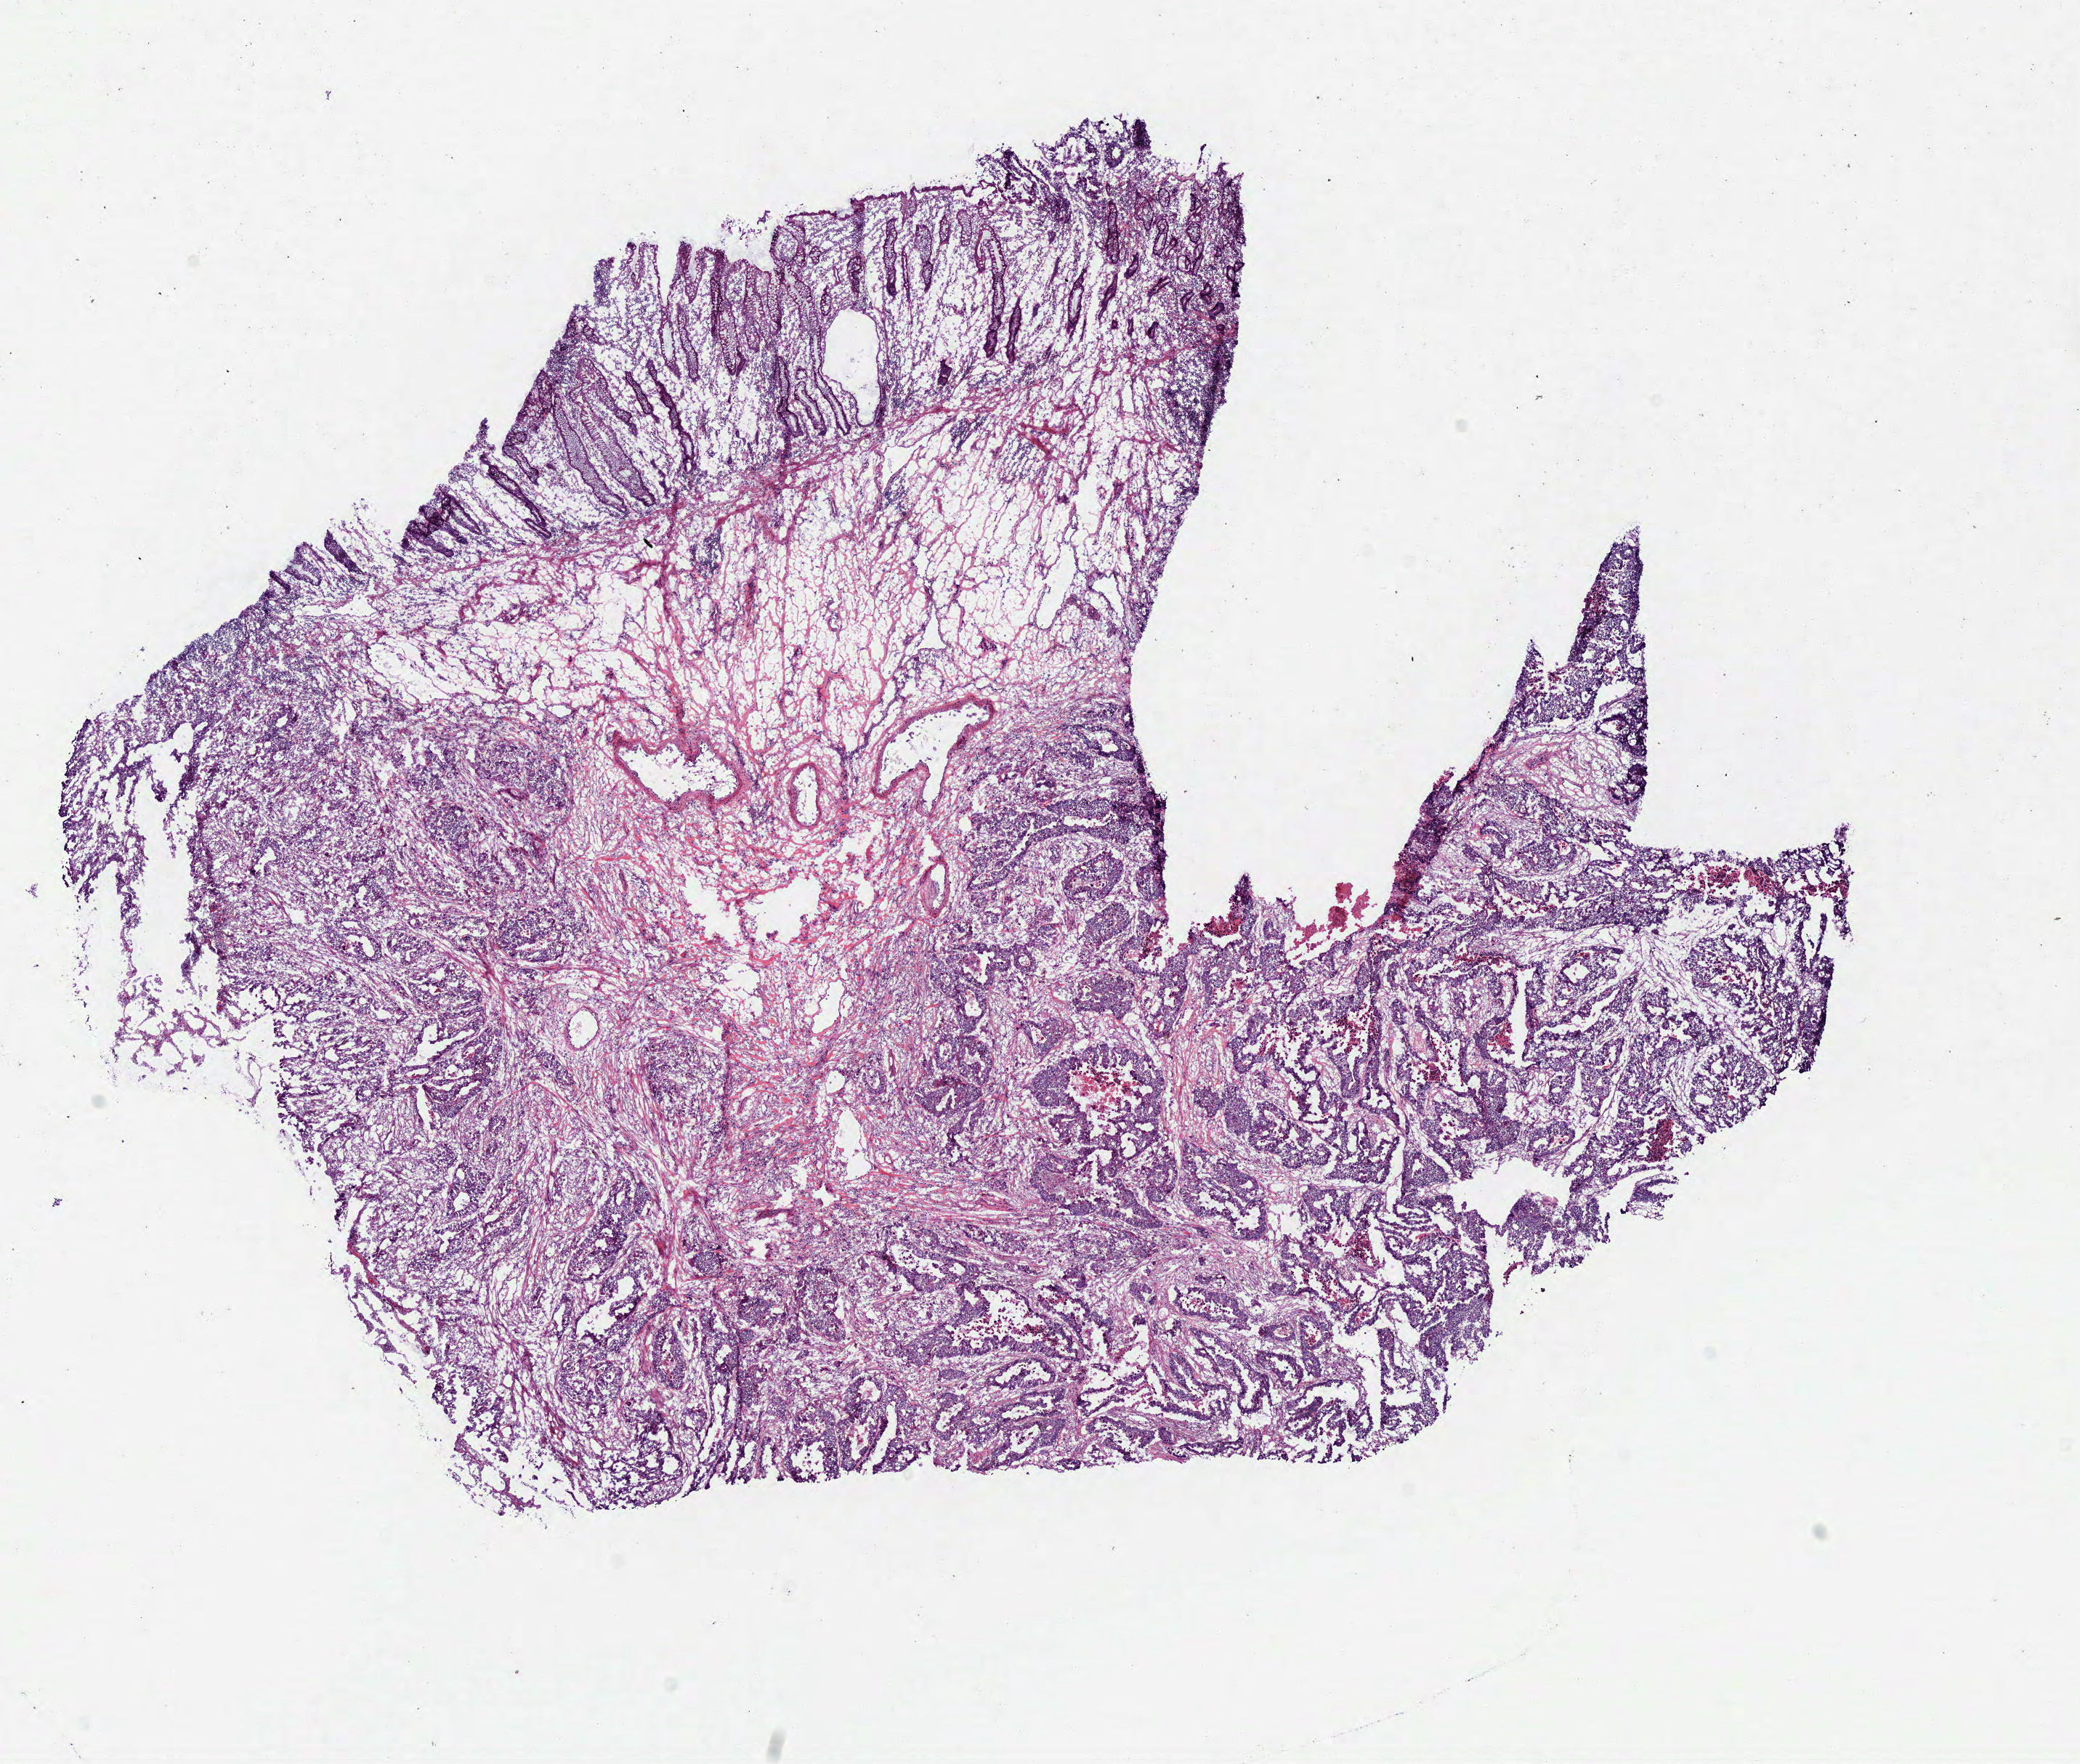
H&E-stained whole-slide image, shown as a low-resolution overview of the whole scanned area (about 11.3 x 9.5 mm, acquisition: 40x scan), frozen section, sample: primary tumour, colon. Female patient; age at initial diagnosis 55 years. Composition of this section per pathologist review: tumour cells 62%, tumour nuclei 80%, normal cells 8%, stromal cells 25%, necrosis 5%.
- lymph nodes positive (case pathology): 6 of 36 examined
- histologic diagnosis: Adenocarcinoma, NOS (cecum)
- AJCC pathologic stage: IV (6th edition)